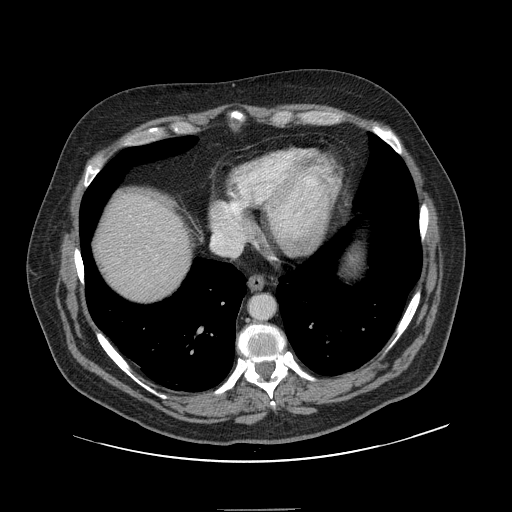
Contrast-enhanced abdominal CT, one axial slice. Slice 137 of 154 in the series (ordered by position). Intravenous contrast given. Soft-tissue window (W 400 / L 40 HU). 2.5 mm slice thickness. 512 × 512 image matrix, field of view 451 × 451 mm. Male patient, age 61 years. Case-level facts recorded for this patient, not image findings: diagnosis: colorectal cancer liver metastases, imaged before liver resection; multiple liver metastases: yes; largest metastasis: 2.6 cm; disease in both lobes: yes.
Structures marked on this image (manually delineated by an expert):
- liver: bounding box [x1, y1, x2, y2] px = [96, 193, 190, 301]
- planned liver remnant (the part of the liver to remain after resection): [96, 193, 190, 301]